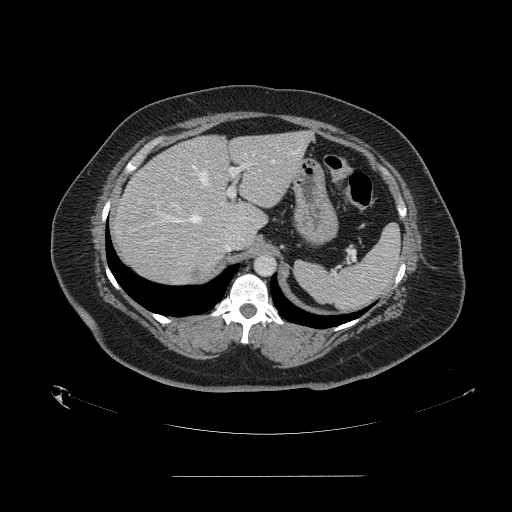
Contrast-enhanced abdominal CT, one axial slice. Slice 109 of 164 in the series (ordered by position). 120 kVp. Soft-tissue window (W 400 / L 40 HU). 2.5 mm slice thickness. 512 × 512 image matrix, field of view 495 × 495 mm. Female patient, age 52 years. From the clinical record (not read from this slice): diagnosis: colorectal cancer liver metastases, imaged before liver resection; multiple liver metastases: yes.
Outlined on this slice (outlined manually by an expert reader):
- hepatic veins: bounding box [x1, y1, x2, y2] px = [162, 150, 298, 223]
- liver: [113, 132, 310, 286]
- planned liver remnant (the part of the liver to remain after resection): [172, 132, 311, 231]
- portal vein (with intrahepatic branches): [171, 163, 250, 209]
- liver metastasis: [191, 266, 204, 278]
- liver metastasis: [250, 208, 260, 221]